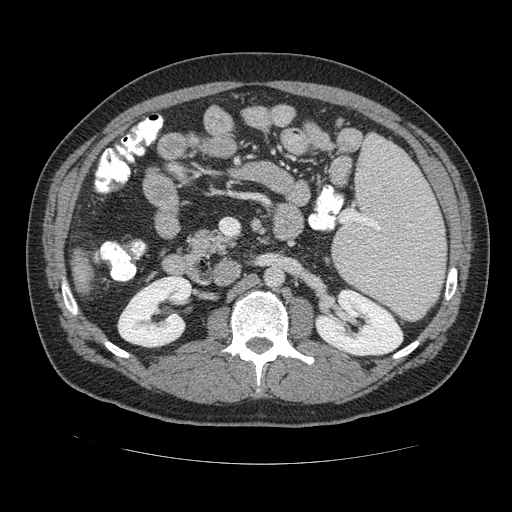
Contrast-enhanced abdominal CT (liver protocol), one axial slice; slice 50 of 113 in the series (ordered by position); reconstruction kernel STANDARD; soft-tissue window (W 400 / L 40 HU); 2.5 mm slice thickness; 512 × 512 image matrix. Case-level facts recorded for this patient, not image findings: diagnosis: hepatocellular carcinoma (patient treated with transarterial chemoembolisation; whether this scan precedes or follows treatment is not stated here); TNM stage (as recorded): Stage-II; Child-Pugh class: B; tumour differentiation: moderately differentiated; tumour nodularity: multinodular.
Structures marked on this image (semi-automatically segmented with operator editing):
- liver parenchyma outside the tumour (the mass and vessels are separate outlines, so this box may not span the whole liver): bounding box (x1, y1, x2, y2) in pixels: (68, 247, 96, 296)